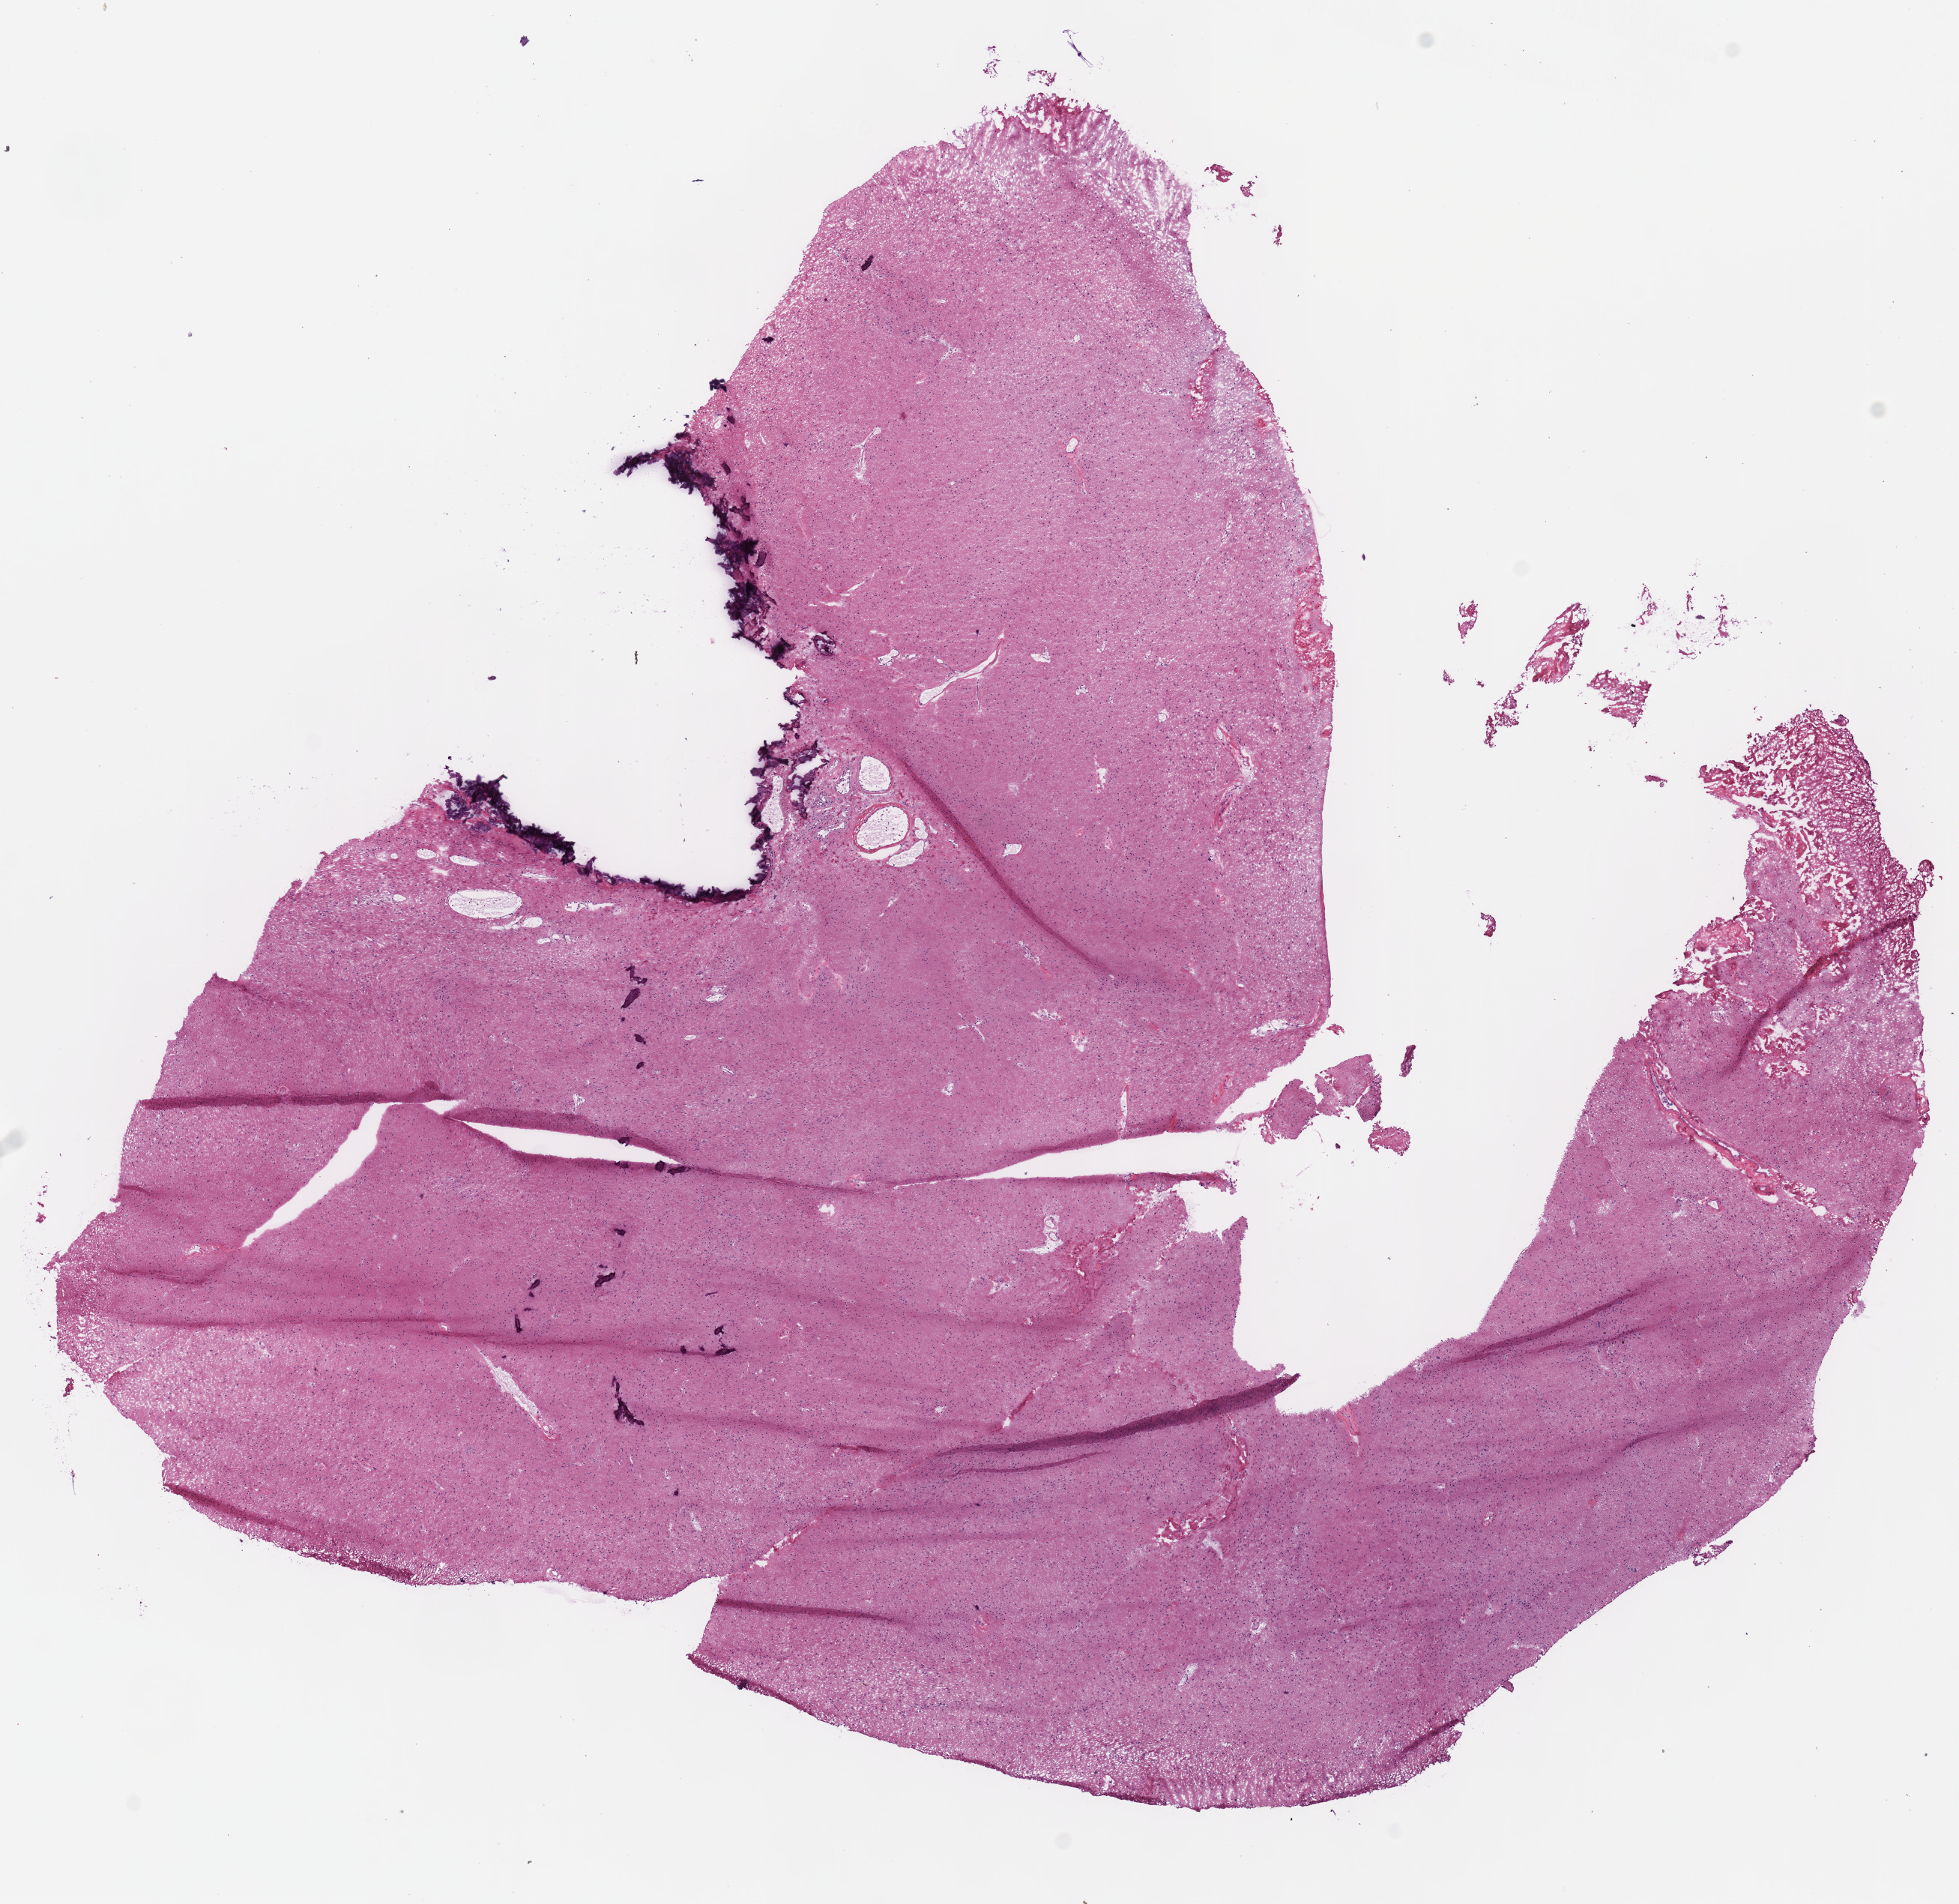
H&E-stained whole-slide image, low-resolution overview of the scanned area, about 10.3 x 10.0 mm; frozen section from the bottom of the tissue portion; primary tumour sample from the brain. Patient: female, age at initial diagnosis 32 years. Histologic grade: G2 (moderately differentiated). Composition of this section per pathologist review: tumour cells 100%, tumour nuclei 65%, normal cells 0%, stromal cells 0%, necrosis 0%.
Histologic diagnosis: Astrocytoma, NOS.